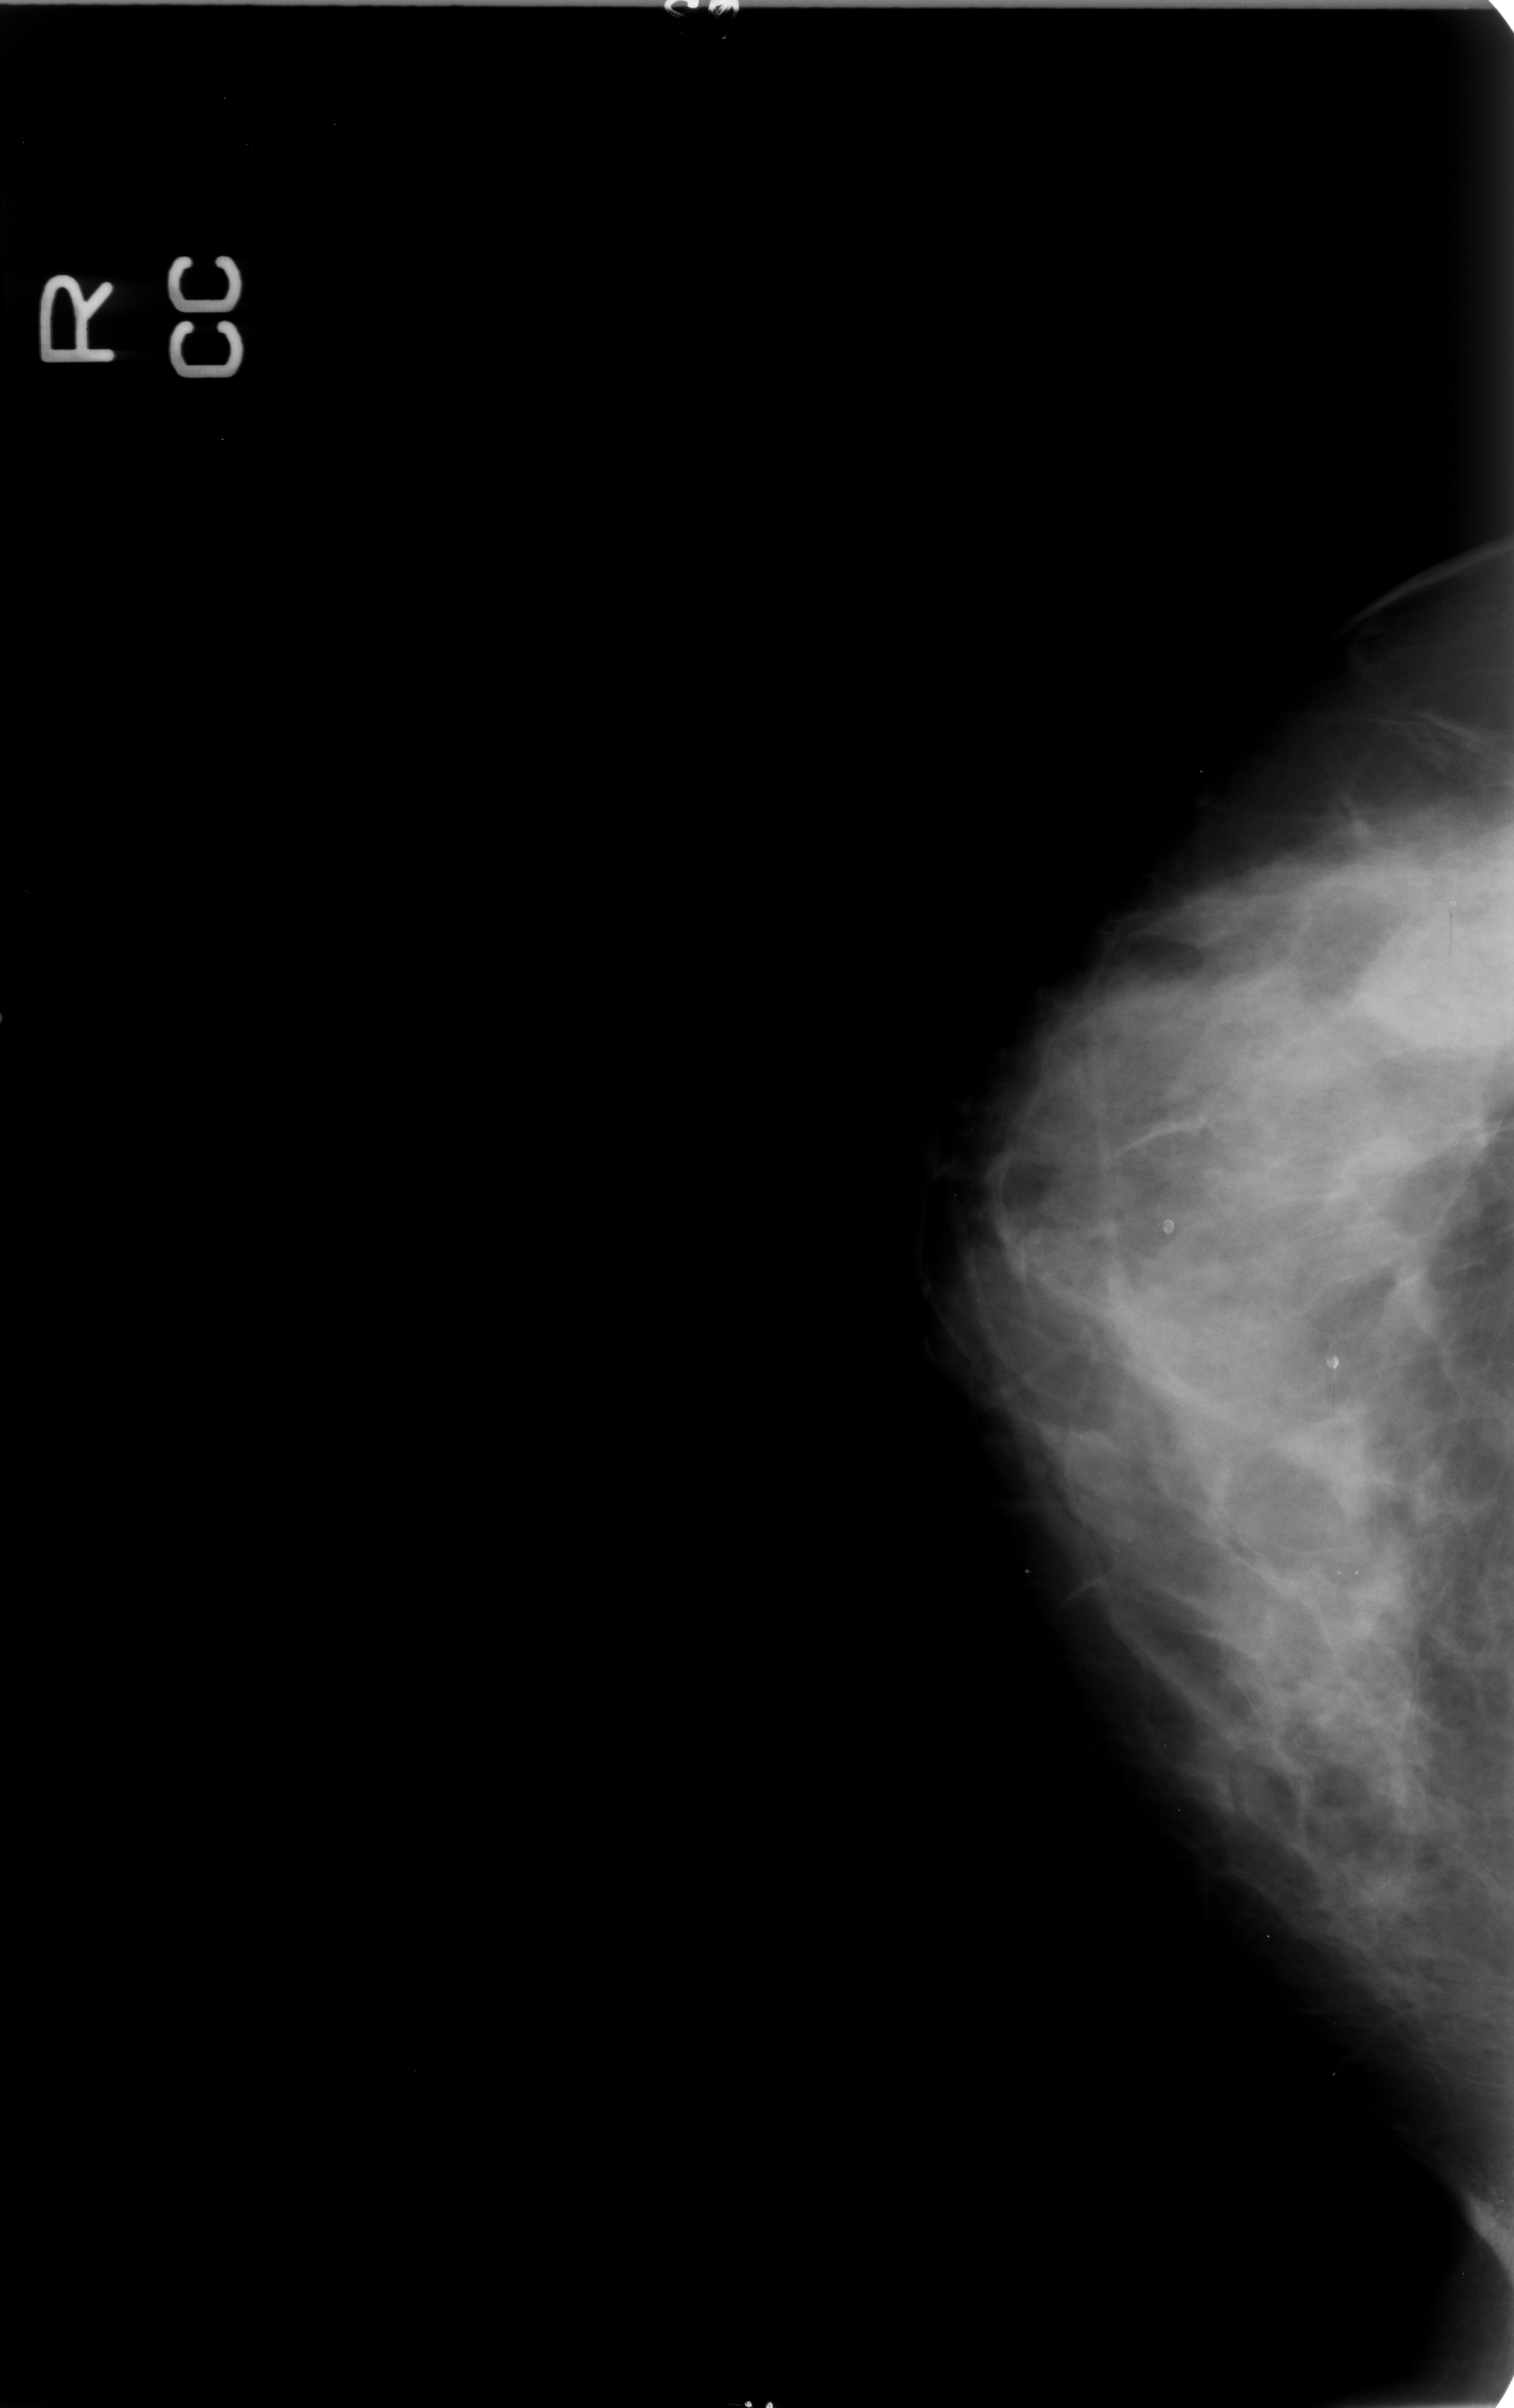
Mammogram (digitized film). Right breast. Craniocaudal (CC) view. Breast composition: heterogeneously dense (BI-RADS density category 3 of 4). 1514 × 2408 image matrix.
Expert-marked regions of interest on this image (one box per marked abnormality):
- Finding 1 of 3: calcifications, morphology round and regular / lucent centered; BI-RADS assessment category 2; subtlety rating 3 on a 1 (subtle) to 5 (obvious) scale; benign; no additional work-up was recommended (outcome (as recorded, no biopsy): benign without callback): bounding box <1143,1201,1186,1249> (left, top, right, bottom; pixels)
- Finding 2 of 3: calcifications, morphology round and regular / lucent centered; BI-RADS assessment category 2; subtlety rating 3 on a 1 (subtle) to 5 (obvious) scale; benign; no additional work-up was recommended (outcome (as recorded, no biopsy): benign without callback): <1306,1335,1353,1382>
- Finding 3 of 3: calcifications, morphology round and regular / lucent centered; BI-RADS assessment category 2; benign; no additional work-up was recommended (outcome (as recorded, no biopsy): benign without callback): <1430,881,1469,928>